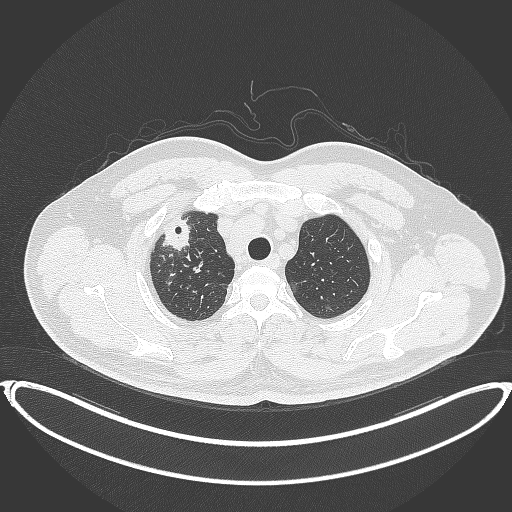
Chest CT, one axial slice; slice 333 of 399 in the series (ordered by position); reconstruction kernel B70f; lung window (W 1500 / L -600 HU); 512 × 512 image matrix, field of view 445 × 445 mm. Patient: male, 53 years. From the clinical record (not read from this slice): clinical TNM (as recorded): T2a N0 M0.
Outlined on this slice (bounding box drawn by a radiologist):
- lung tumour (recorded histology: adenocarcinoma): box from (x=162, y=216) to (x=194, y=257) px